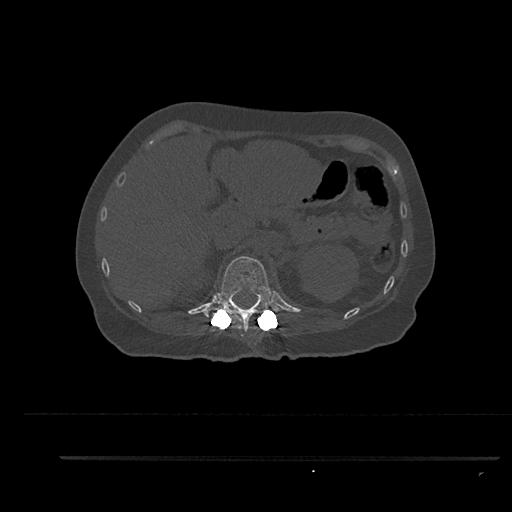
CT including the spine, one axial slice; position 262 of 797 along the scan axis; reconstruction kernel Br40s/3; 120 kVp; bone window (W 1800 / L 400 HU); 0.5 mm slice thickness; 512 × 512 image matrix. Patient: female, 44 years. Case-level facts recorded for this patient, not image findings: primary cancer: renal.
Structures marked on this image (semi-automatic segmentation, software-assisted and operator-edited):
- T12 vertebra: bounding box <204,256,282,332> (left, top, right, bottom; pixels)